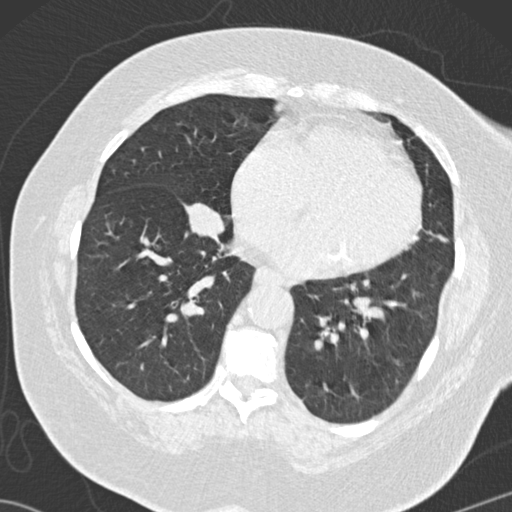
Low-dose screening chest CT, one axial slice; slice 52 of 146 in the series (ordered by position); reconstruction kernel B30f; 120 kVp; lung window (W 1500 / L -600 HU); 512 × 512 image matrix.
Outlined on this slice (manually delineated by an expert):
- lesion 3 (tumor, lower lobe of right lung): bounding box (x1, y1, x2, y2) in pixels: (191, 203, 224, 236)